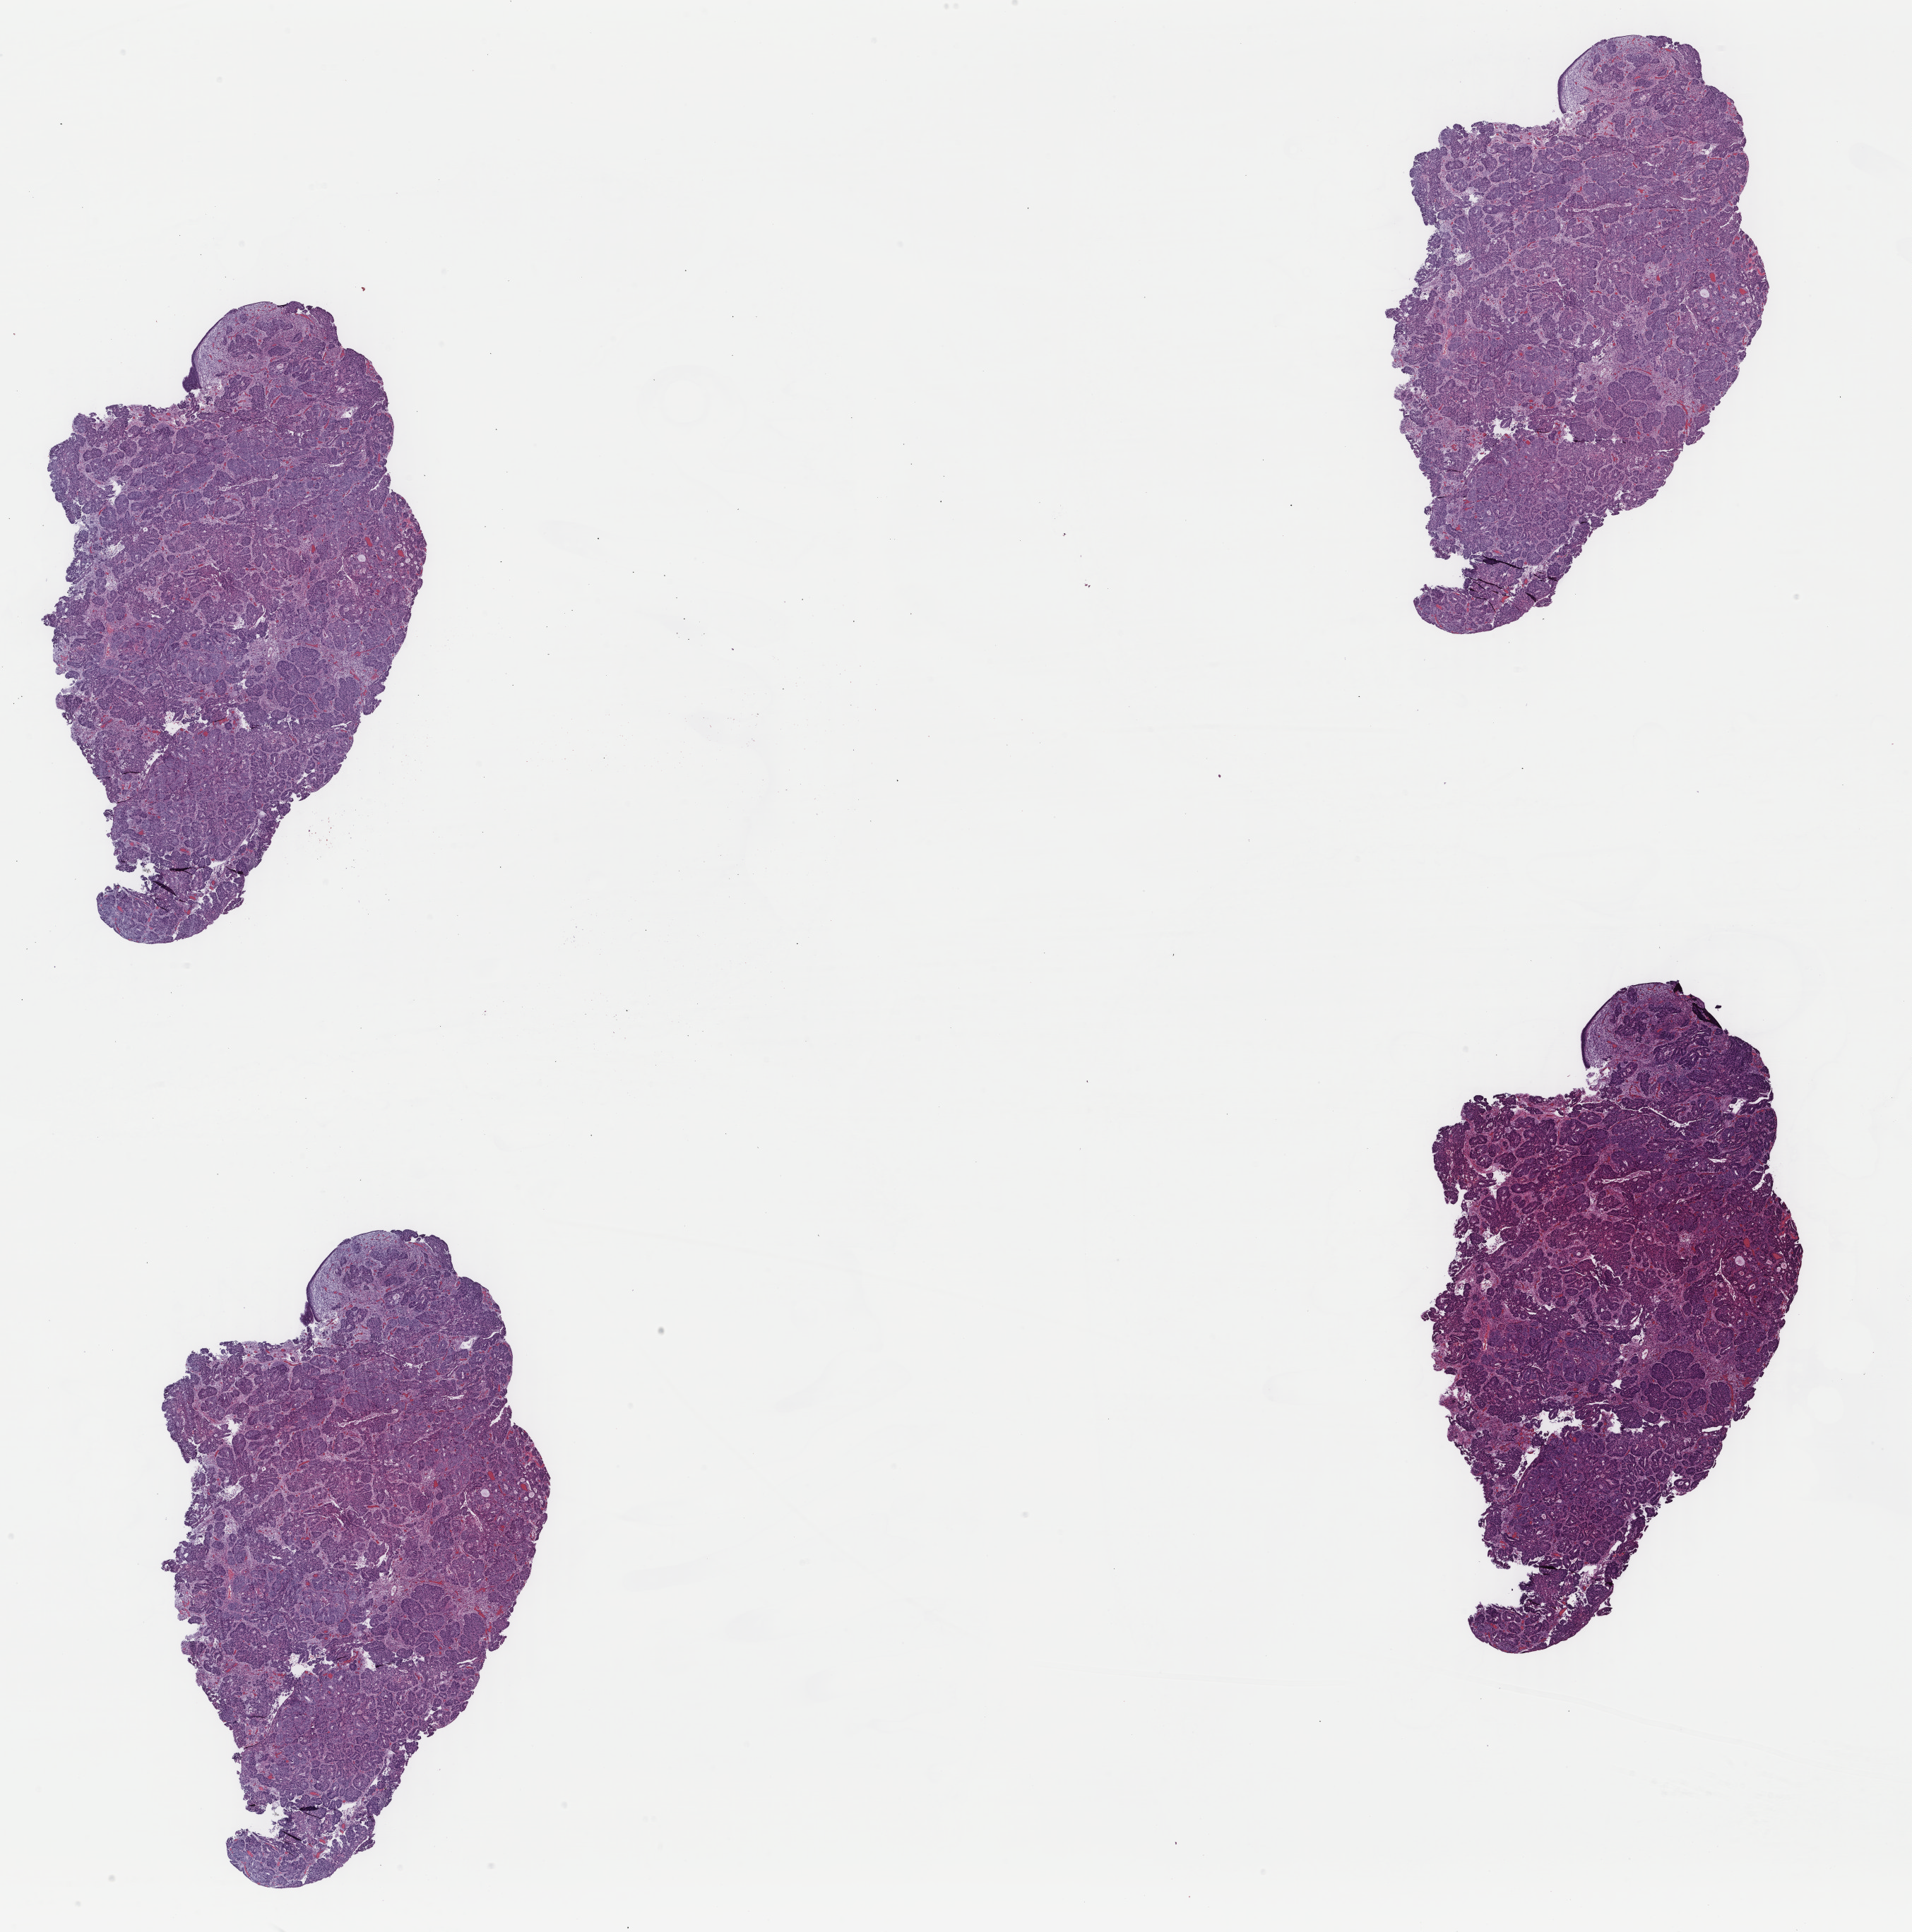
H&E whole-slide image — low-resolution overview of the scanned area, about 21.5 x 21.7 mm. Formalin-fixed paraffin-embedded (FFPE) diagnostic section. Uterus, primary tumour sample. Patient: female, age at initial diagnosis 42 years. Histologic grade: G3 (poorly differentiated).
FIGO stage: IA. Pathologic diagnosis: Endometrioid adenocarcinoma, NOS.